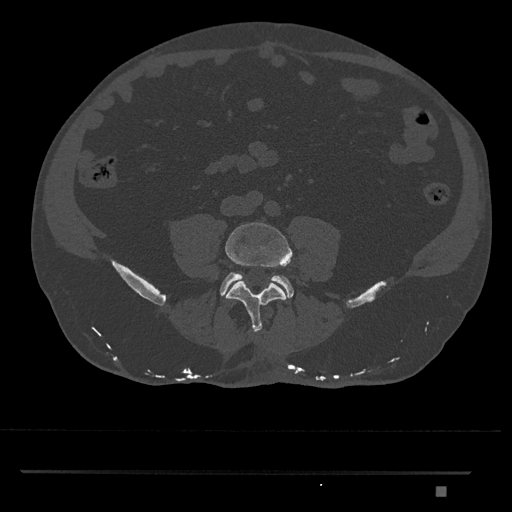
CT including the spine, one axial slice; position 595 of 1134 along the scan axis; 120 kVp; bone window (W 1800 / L 400 HU); 0.5 mm slice thickness; 512 × 512 image matrix, field of view 429 × 429 mm. Male patient, age 65 years. Case-level facts recorded for this patient, not image findings: primary cancer: prostate.
Outlined on this slice (semi-automatic segmentation, software-assisted and operator-edited):
- L4 vertebra: bounding box [x1, y1, x2, y2] px = [225, 222, 293, 333]
- L5 vertebra: [220, 272, 294, 298]